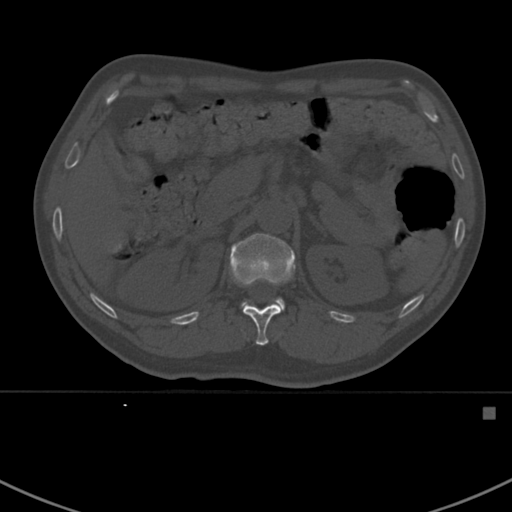
CT including the spine, one axial slice. Position 321 of 412 along the scan axis. Reconstruction kernel Br40s. Bone window (W 1800 / L 400 HU). 1.5 mm slice thickness. 512 × 512 image matrix, field of view 358 × 358 mm. Patient: male, 59 years. From the clinical record (not read from this slice): primary cancer: prostate.
Structures marked on this image (semi-automatically segmented with operator editing):
- L1 vertebra: bounding box (x1, y1, x2, y2) in pixels: (230, 233, 296, 311)
- T12 vertebra: (242, 304, 281, 346)